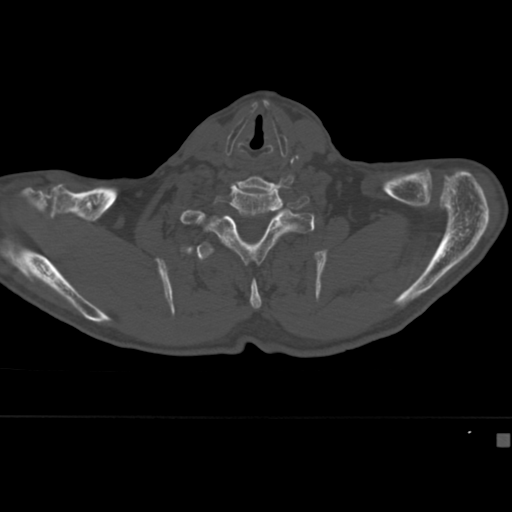
CT including the spine, one axial slice; slice 353 of 430 in the series (ordered by position); reconstruction kernel Br40s; 120 kVp; bone window (W 1800 / L 400 HU); 512 × 512 image matrix, field of view 337 × 337 mm. Patient: male, 64 years. Case-level facts recorded for this patient, not image findings: primary cancer: uterus; vertebrae with lytic lesions (as recorded): T1, T4, T5, T7, L5.
Outlined on this slice (semi-automatic segmentation, software-assisted and operator-edited):
- T2 vertebra: bounding box <196,242,261,310> (left, top, right, bottom; pixels)